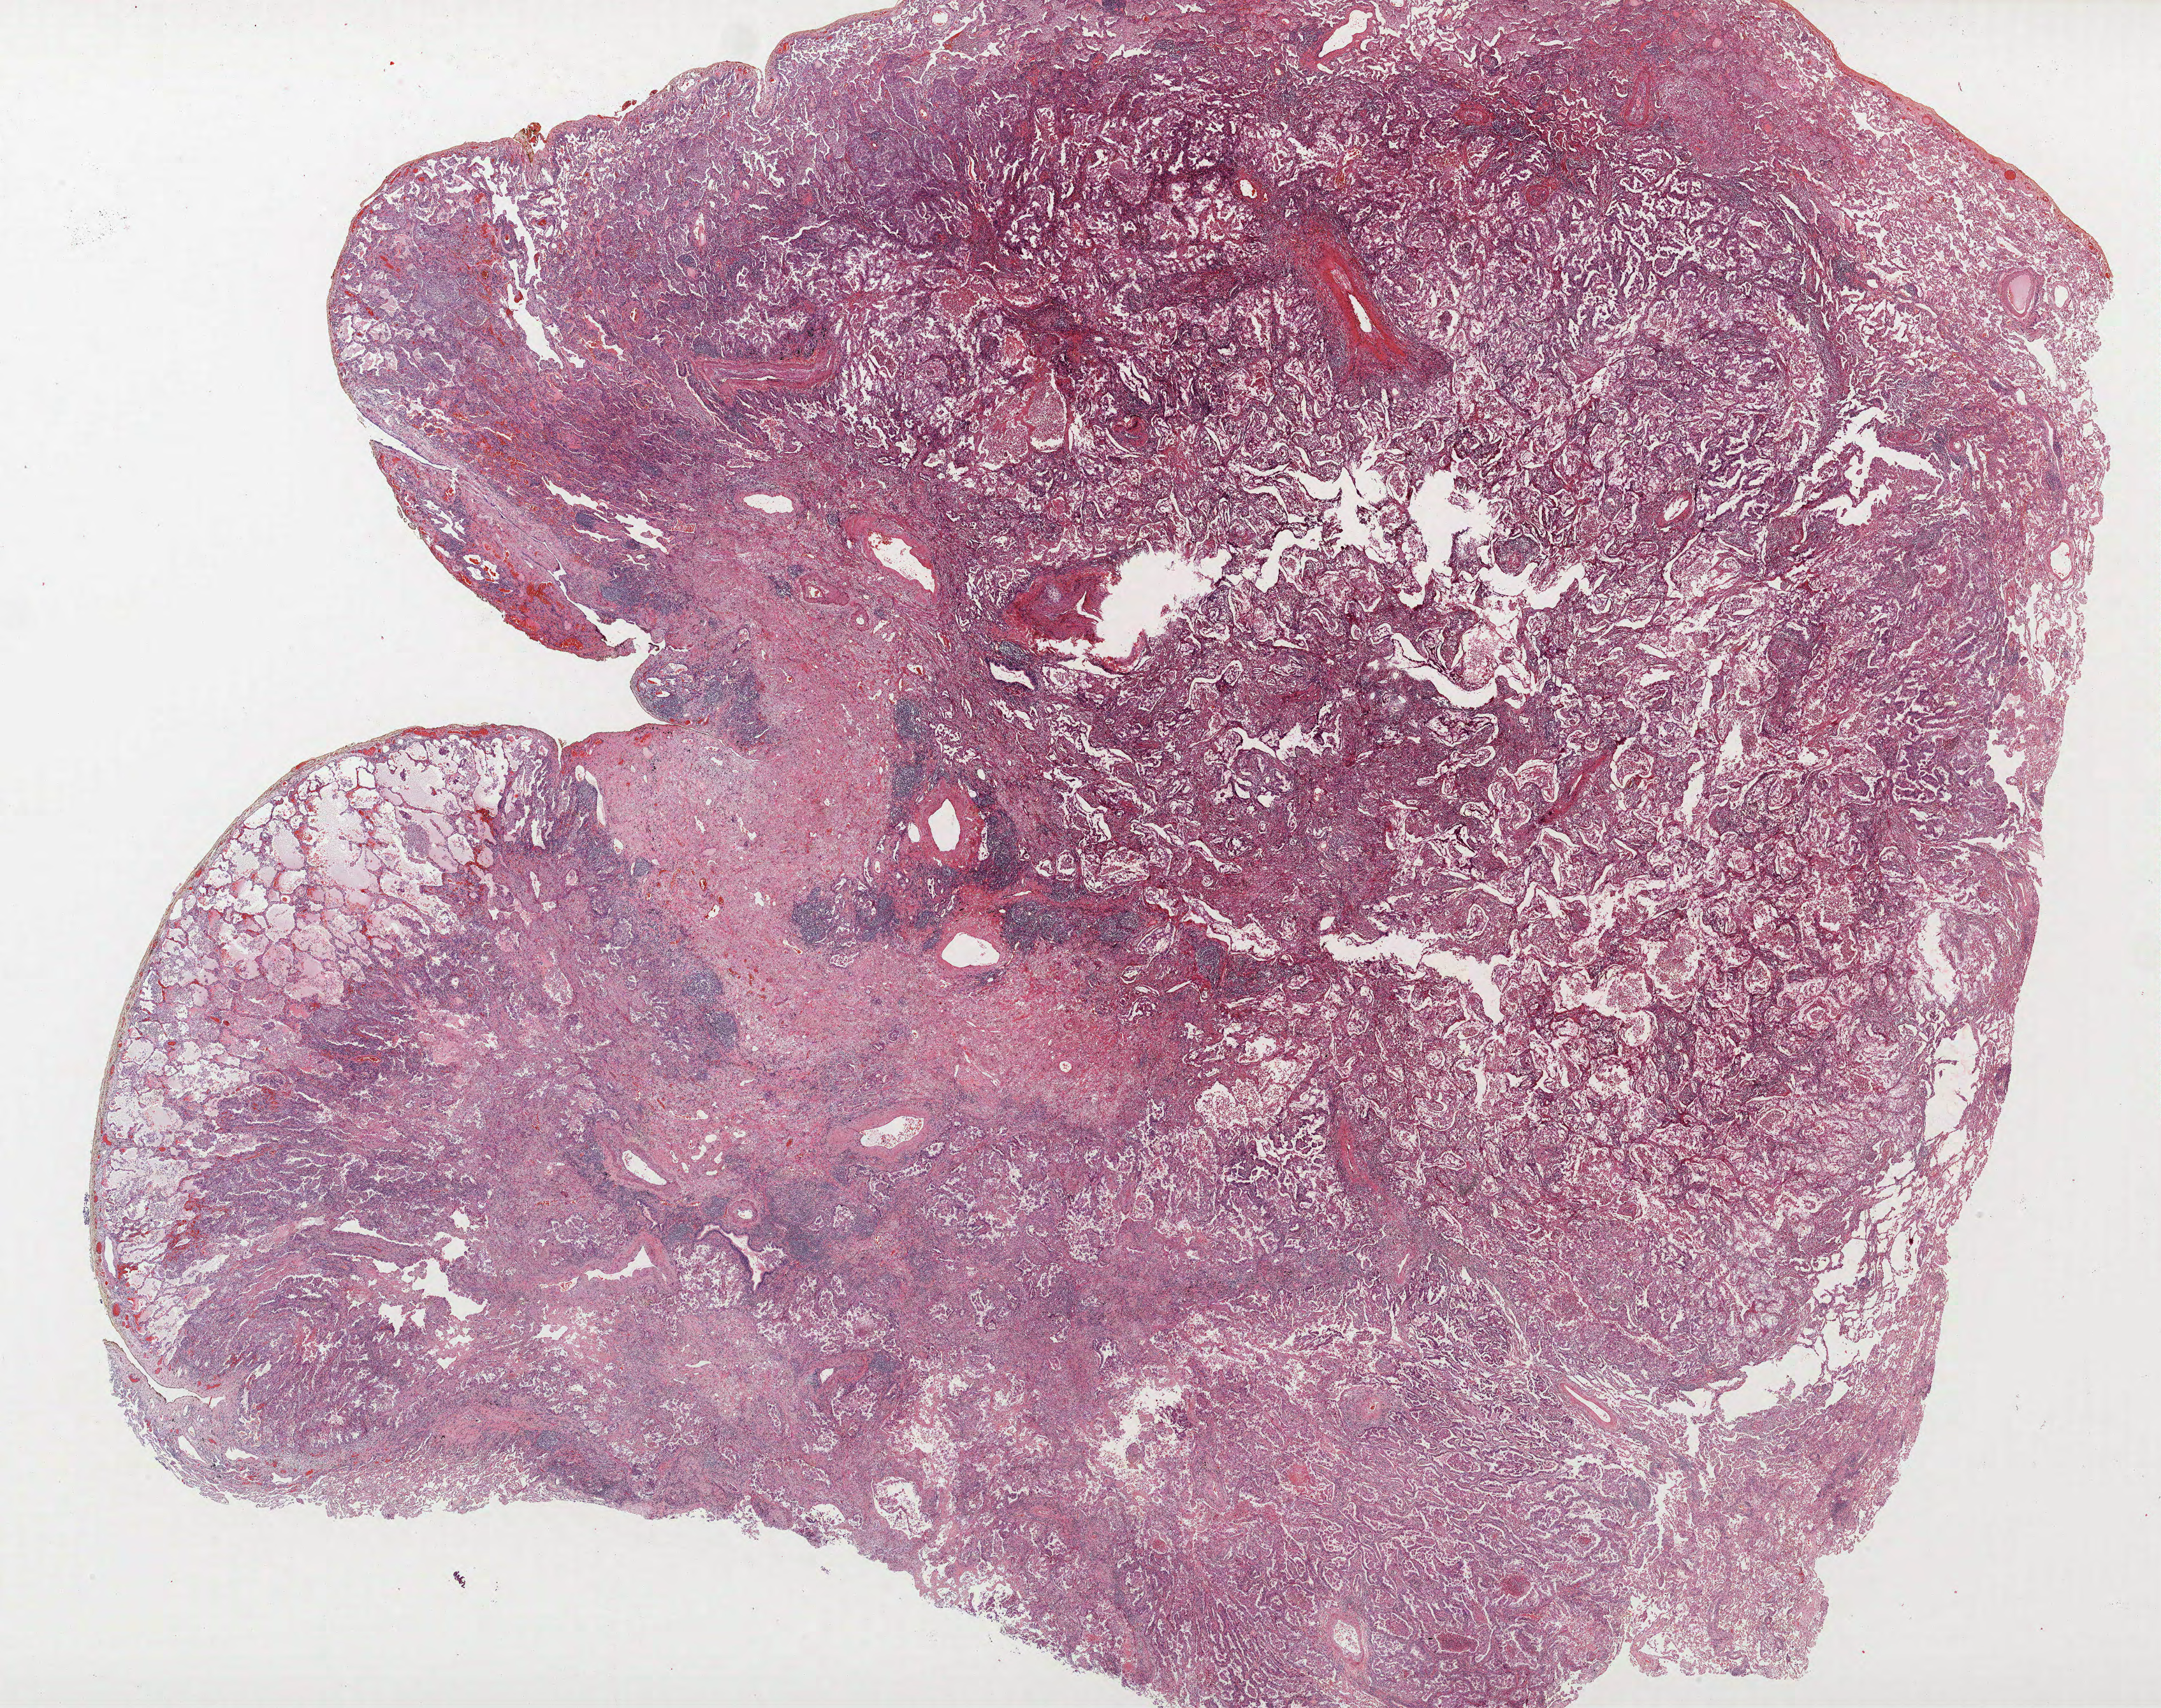
Whole-slide histology image, Hematoxylin and eosin (H&E) stained, whole scanned area (about 27.1 x 21.4 mm, from a 40x scan) shown as a low-resolution overview. FFPE section. Lung. Female, age 58 at enrolment. Former smoker at enrolment. Grade: poorly differentiated (G3).
• ICD-O-3 topography: upper lobe of lung (C34.1)
• participant's lung-cancer diagnosis: Acinar cell carcinoma (ICD-O-3 8550/3)
• primary tumour location (clinical record): left upper lobe
• tumour size (pathology): 37 mm
• stage (AJCC 6th edition): IIIA